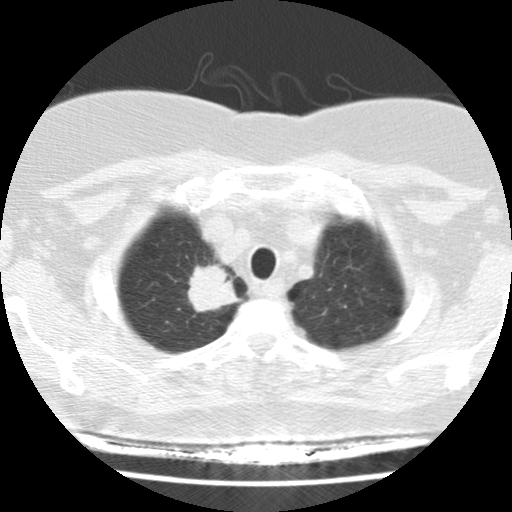
Low-dose screening chest CT, axial slice, baseline annual screen, lung window (W 1500 / L -600 HU), 2.5 mm slice thickness, standard (soft-tissue) reconstruction kernel (STANDARD), 120 kVp. Female, age 58 years at enrolment. Former smoker at enrolment.
- Expert-annotated lung lesion, bounding box <169,250,247,327> (left, top, right, bottom; pixels).
- Screening reader's record for this exam (one nodule recorded; not confirmed to be the boxed lesion): non-calcified nodule or mass ≥4 mm, right upper lobe, 28 × 24 mm, spiculated (stellate) margins, soft tissue attenuation.
- Official screen result: positive, change unspecified: nodule(s) >= 4 mm or enlarging nodule(s), mass(es), or other non-specific abnormalities suspicious for lung cancer.